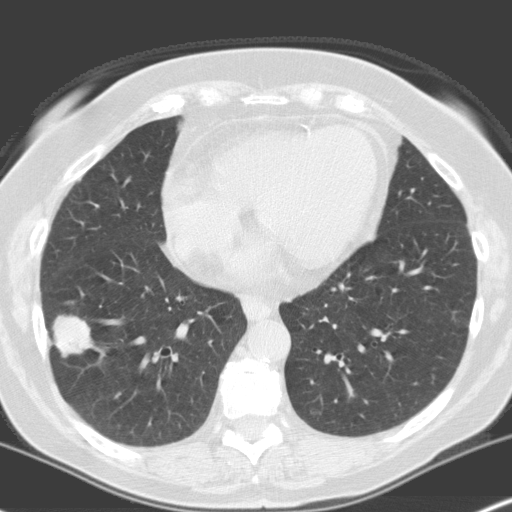
Low-dose screening chest CT, one axial slice; slice 68 of 160 in the series (ordered by position); 120 kVp; lung window (W 1500 / L -600 HU); 512 × 512 image matrix, field of view 316 × 316 mm.
Annotated regions visible in this slice (manually delineated by an expert):
- lesion 1 (tumor, lower lobe of right lung): bounding box <52,315,93,358> (left, top, right, bottom; pixels)